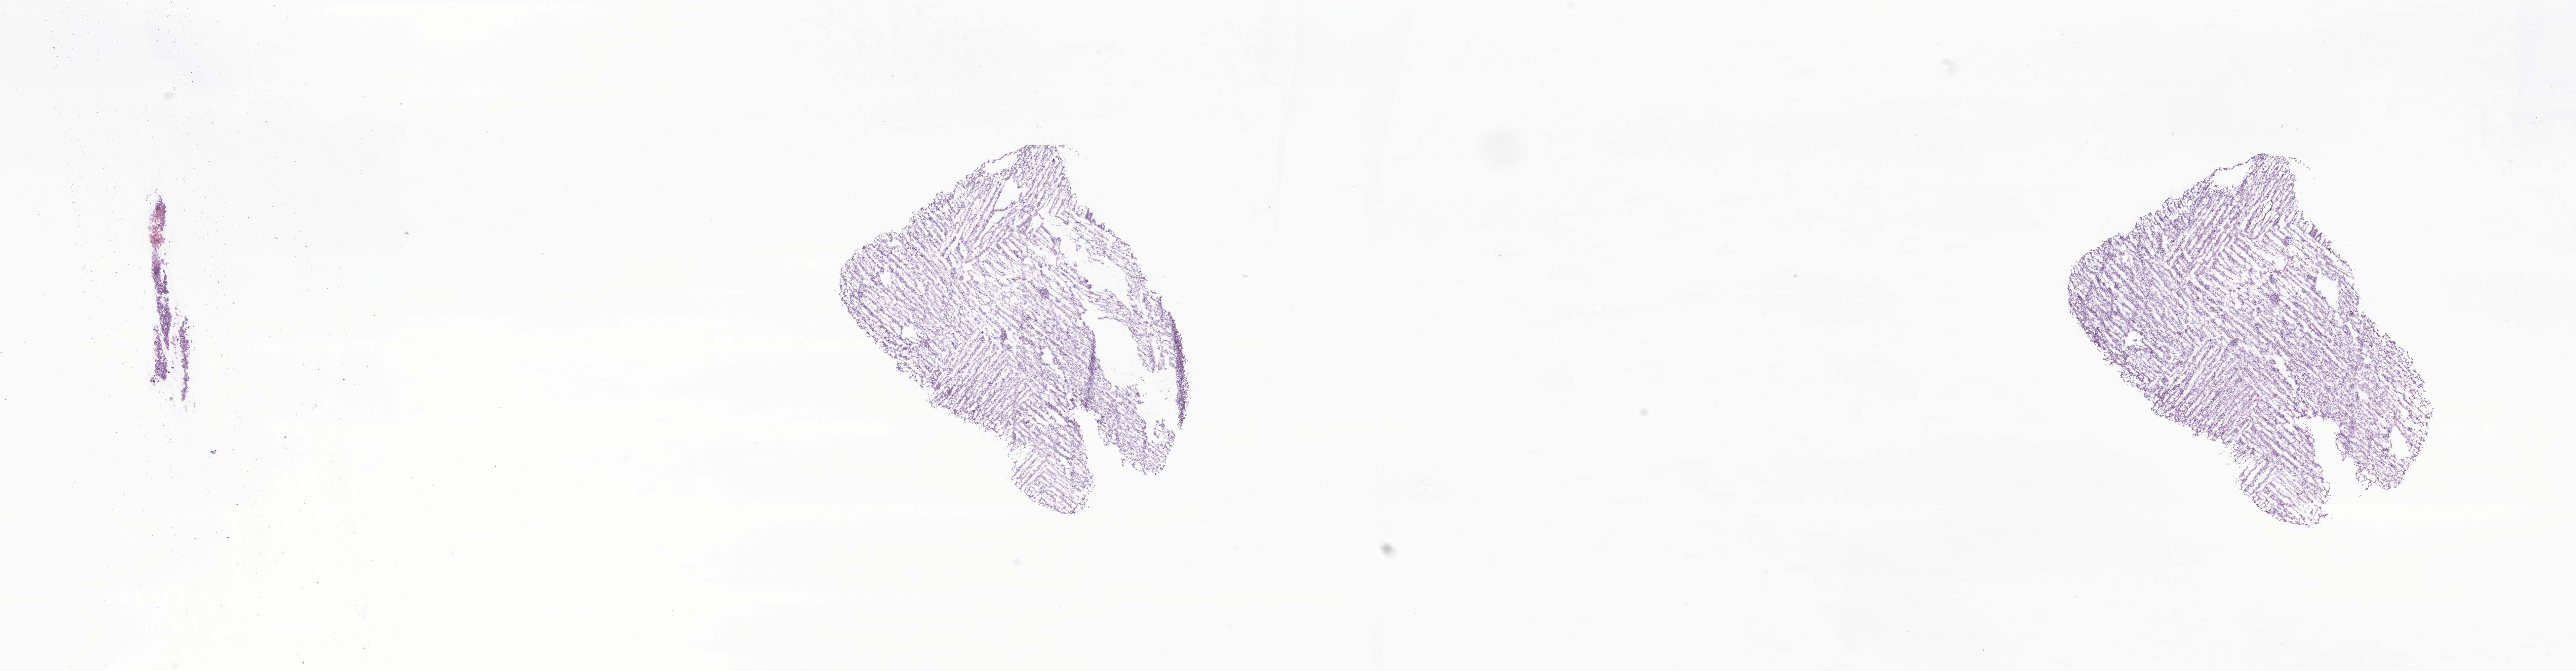
Digitized haematoxylin and eosin-stained section of tumor tissue from the brain, low-resolution overview of the scanned area, about 32.9 x 8.6 mm. Frozen section (OCT-embedded). Patient female; age 34 months (2 years 10 months).
• recorded diagnosis: Glioma, malignant